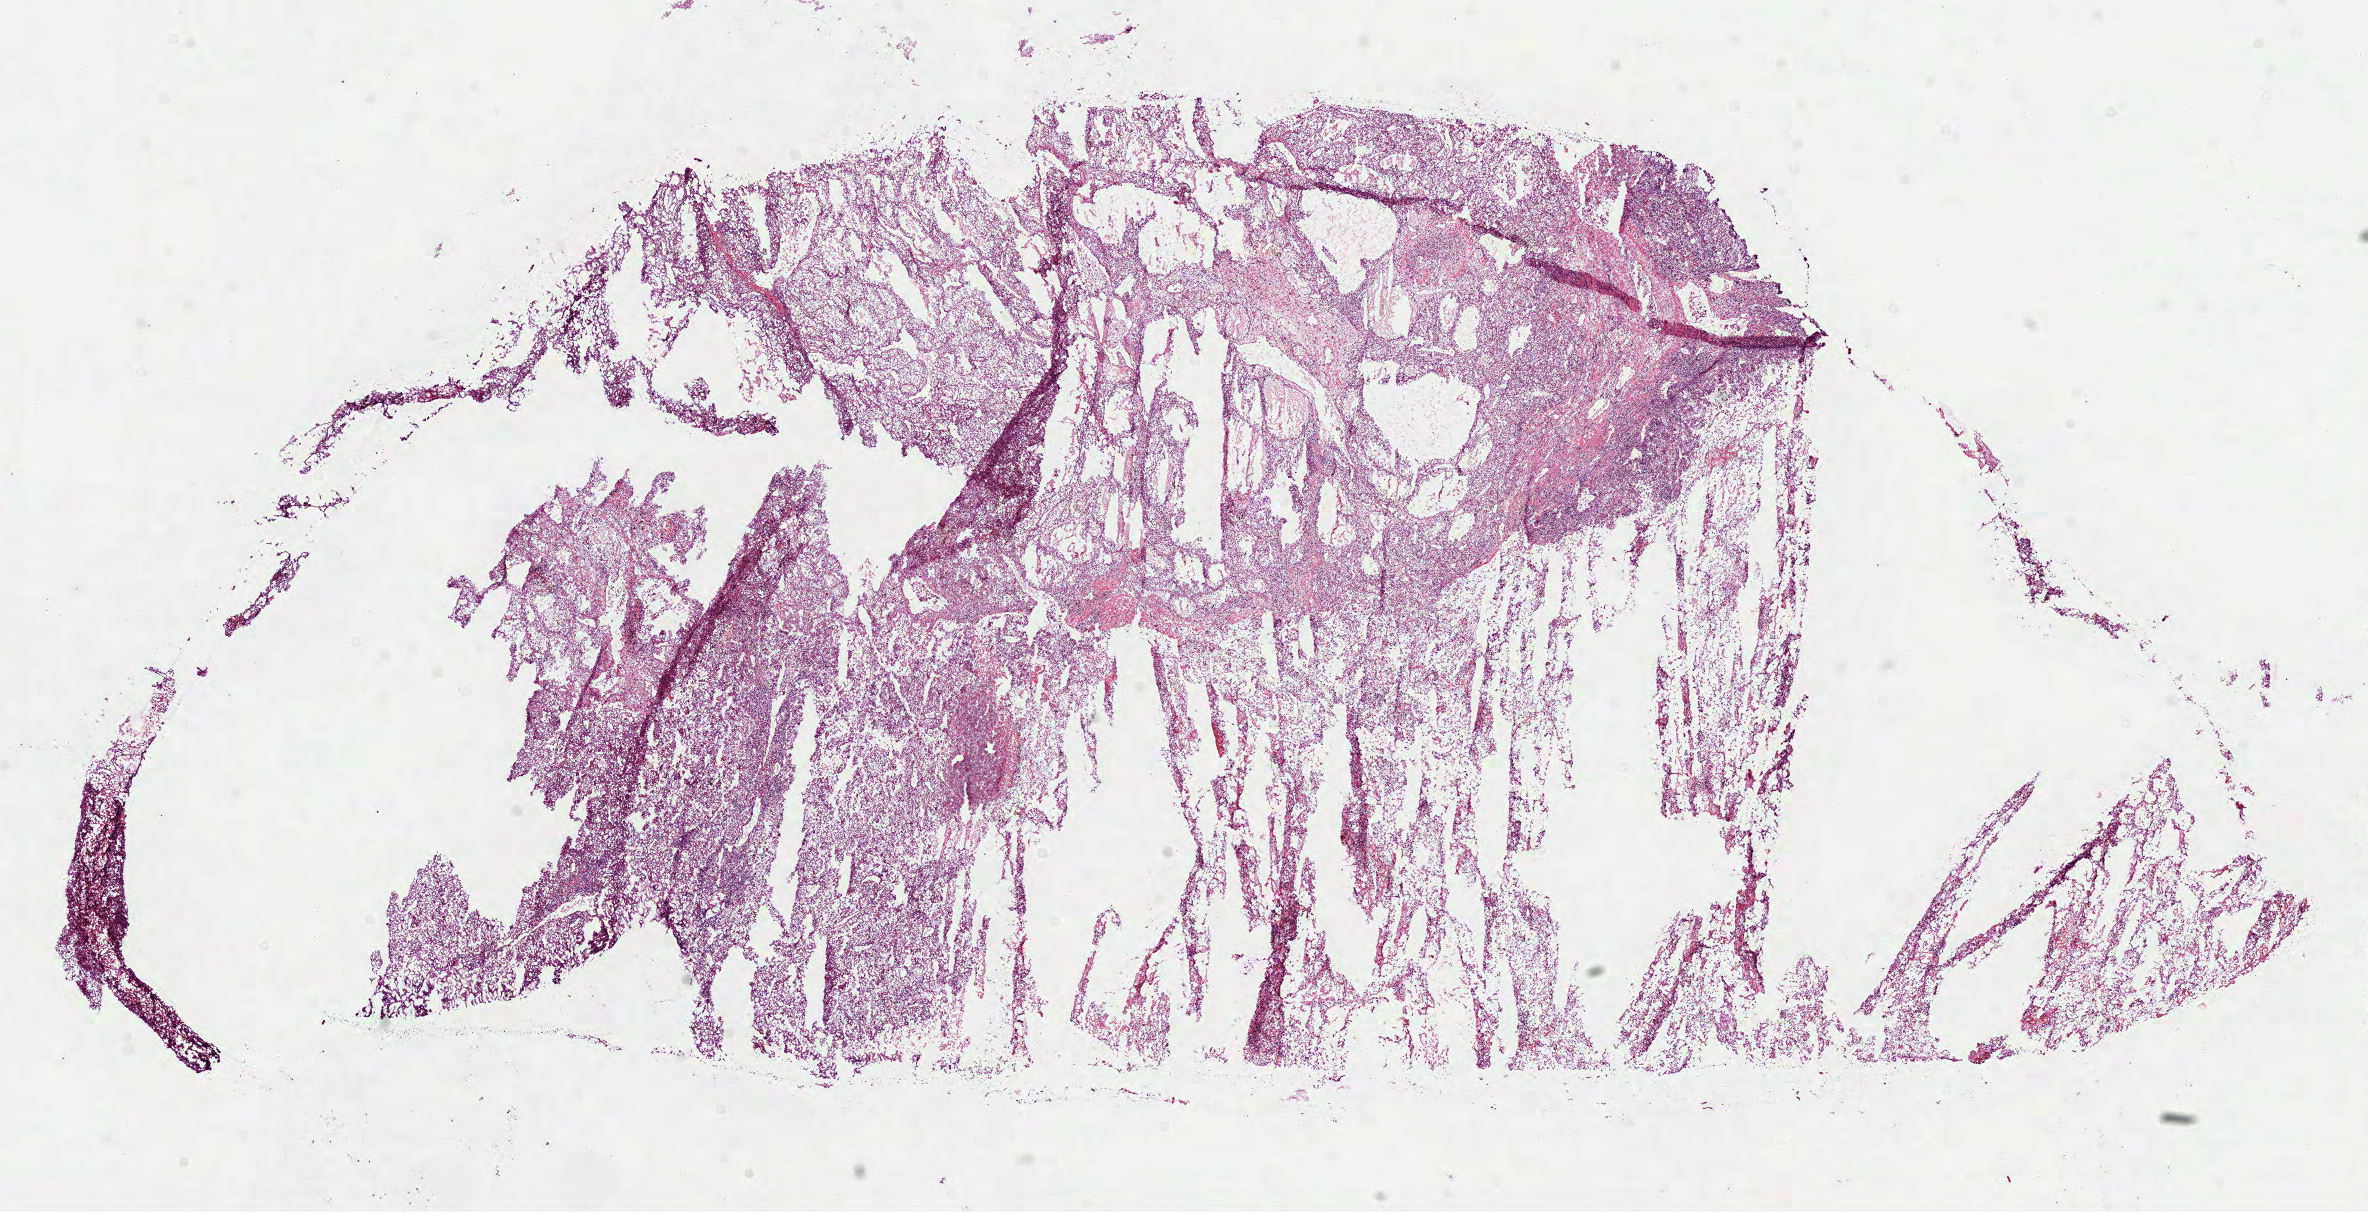
Hematoxylin and eosin (H&E) stained whole-slide image, low-resolution overview of the scanned area, about 19.1 x 9.8 mm. Frozen section from the bottom of the tissue portion. Primary tumour sample from the kidney. Male patient; age at initial diagnosis 58 years. Histologic grade: G4 (undifferentiated). Slide review estimates, as recorded: tumour cells 85%, tumour nuclei 70%, normal cells 0%, stromal cells 15%, necrosis 0%. Infiltration values recorded for this section: lymphocyte infiltration 20%, monocyte infiltration 3%, neutrophil infiltration 1%.
* diagnosis: Clear cell adenocarcinoma, NOS
* laterality: left
* AJCC pathologic stage: IV